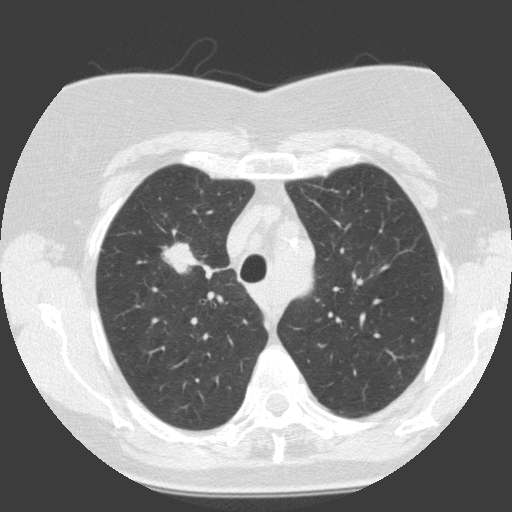
Axial slice from a low-dose chest CT screening exam. Baseline annual screen. Lung window (W 1500 / L -600 HU). Standard (soft-tissue) reconstruction kernel (C). Slice 39 of 146 in the series. 512 × 512 image matrix, field of view 300 × 300 mm. Female, age 68 years at enrolment.
• Expert reader's lesion annotation, bounding box (x1, y1, x2, y2) in pixels: (156, 235, 207, 282).
• Reader record for this screening exam (exam-level; its link to the box is not recorded): non-calcified nodule or mass ≥4 mm, right upper lobe, 19 × 12 mm, smooth margins, soft tissue attenuation.
• Later outcome: lung cancer diagnosed 30 days after this screen — squamous cell carcinoma, NOS, right upper lobe, moderately differentiated (G2), stage IA (AJCC 6th edition), 28 mm at pathology.